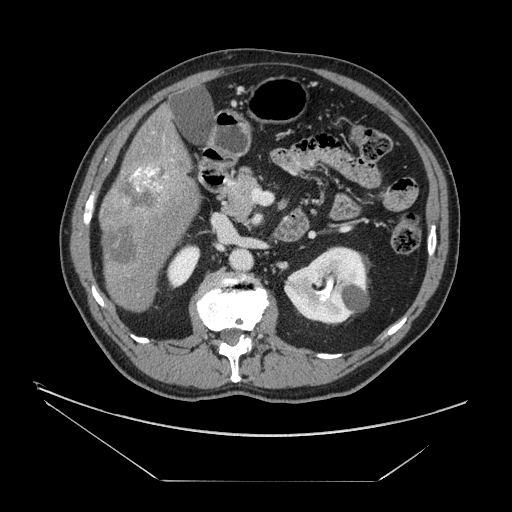
Contrast-enhanced abdominal CT, one axial slice; slice 68 of 161 in the series (ordered by position); reconstruction kernel STANDARD; intravenous contrast given; soft-tissue window (W 400 / L 40 HU); 512 × 512 image matrix, field of view 440 × 440 mm. Male patient, age 65 years. Case-level facts recorded for this patient, not image findings: diagnosis: colorectal cancer liver metastases, imaged before liver resection; multiple liver metastases: yes; largest metastasis: 4.2 cm.
Outlined on this slice (expert manual segmentation):
- liver: box from (x=101, y=109) to (x=200, y=312) px
- portal vein (with intrahepatic branches): (x=133, y=160)–(x=173, y=191)
- liver metastasis: (x=105, y=229)–(x=138, y=266)
- liver metastasis: (x=118, y=167)–(x=170, y=210)